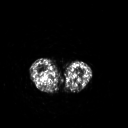
FDG PET of an extremity soft-tissue mass (from a PET/CT study), one axial slice; position 187 of 267 along the scan axis; 3.27 mm slice thickness; 128 × 128 image matrix. Patient: female, 62 years. Case-level facts recorded for this patient, not image findings: histological type: liposarcoma; site of the primary tumour: right thigh.
Structures marked on this image (expert contour drawn on MRI and transferred to this co-registered scan by the dataset authors):
- gross tumour volume (mass): bounding box <44,77,51,82> (left, top, right, bottom; pixels)